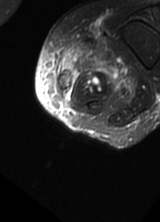
MRI of an extremity soft-tissue mass, one axial slice. Position 7 of 69 along the scan axis. T2-weighted fat-saturated. MR volume resampled by the dataset authors to the PET/CT grid (not the native acquisition matrix). 3.27 mm slice thickness. 160 × 222 image matrix, field of view 156 × 217 mm. Female patient. From the clinical record (not read from this slice): histological type: pleomorphic leiomyosarcoma; grade: high; site of the primary tumour: left thigh.
Structures marked on this image (expert contour drawn on MRI and transferred to this co-registered scan by the dataset authors):
- gross tumour volume including surrounding oedema: bounding box [x1, y1, x2, y2] px = [55, 36, 135, 99]